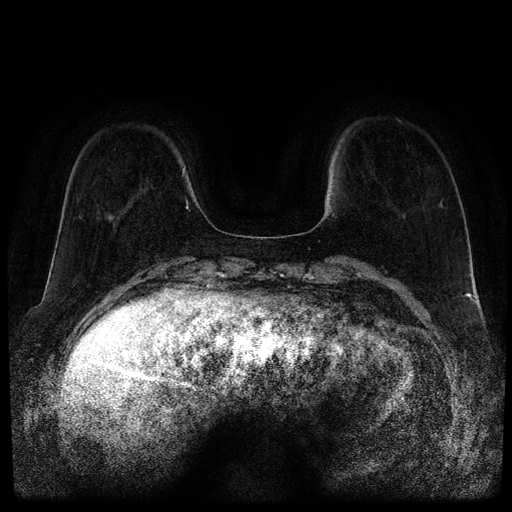
Breast MRI (dynamic contrast-enhanced, multi-phase), one axial slice; dynamic contrast-enhanced series, time point 2 of 5 at this slice position (early post-contrast); 1.5 T; TE 2.6 ms, TR 5.3 ms; 512 × 512 image matrix. Female patient, age 66 years.
Outlined on this slice (semi-automatically segmented with operator editing):
- breast lesion (labelled benign in the annotation): box from (x=107, y=215) to (x=114, y=221) px